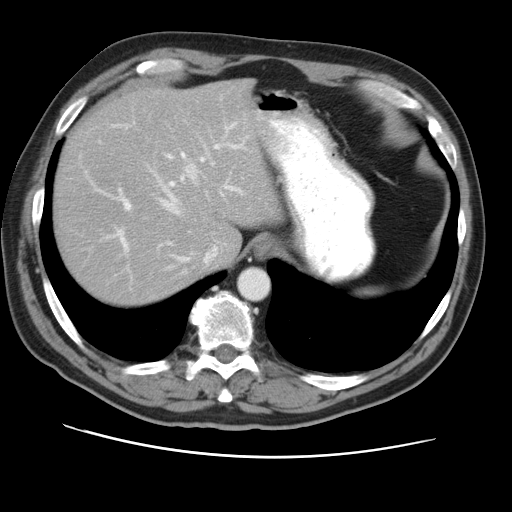
Contrast-enhanced abdominal CT, one axial slice. Slice 38 of 49 in the series (ordered by position). Reconstruction kernel STANDARD. 120 kVp. Intravenous contrast given. Soft-tissue window (W 400 / L 40 HU). 512 × 512 image matrix, field of view 374 × 374 mm. Male patient, age 59 years. From the clinical record (not read from this slice): diagnosis: colorectal cancer liver metastases, imaged before liver resection; multiple liver metastases: yes; largest metastasis: 6.3 cm; disease in both lobes: yes.
Structures marked on this image (manually delineated by an expert):
- hepatic veins: bounding box [x1, y1, x2, y2] px = [152, 124, 248, 269]
- liver: [55, 81, 278, 304]
- planned liver remnant (the part of the liver to remain after resection): [55, 80, 278, 304]
- portal vein (with intrahepatic branches): [84, 124, 242, 257]